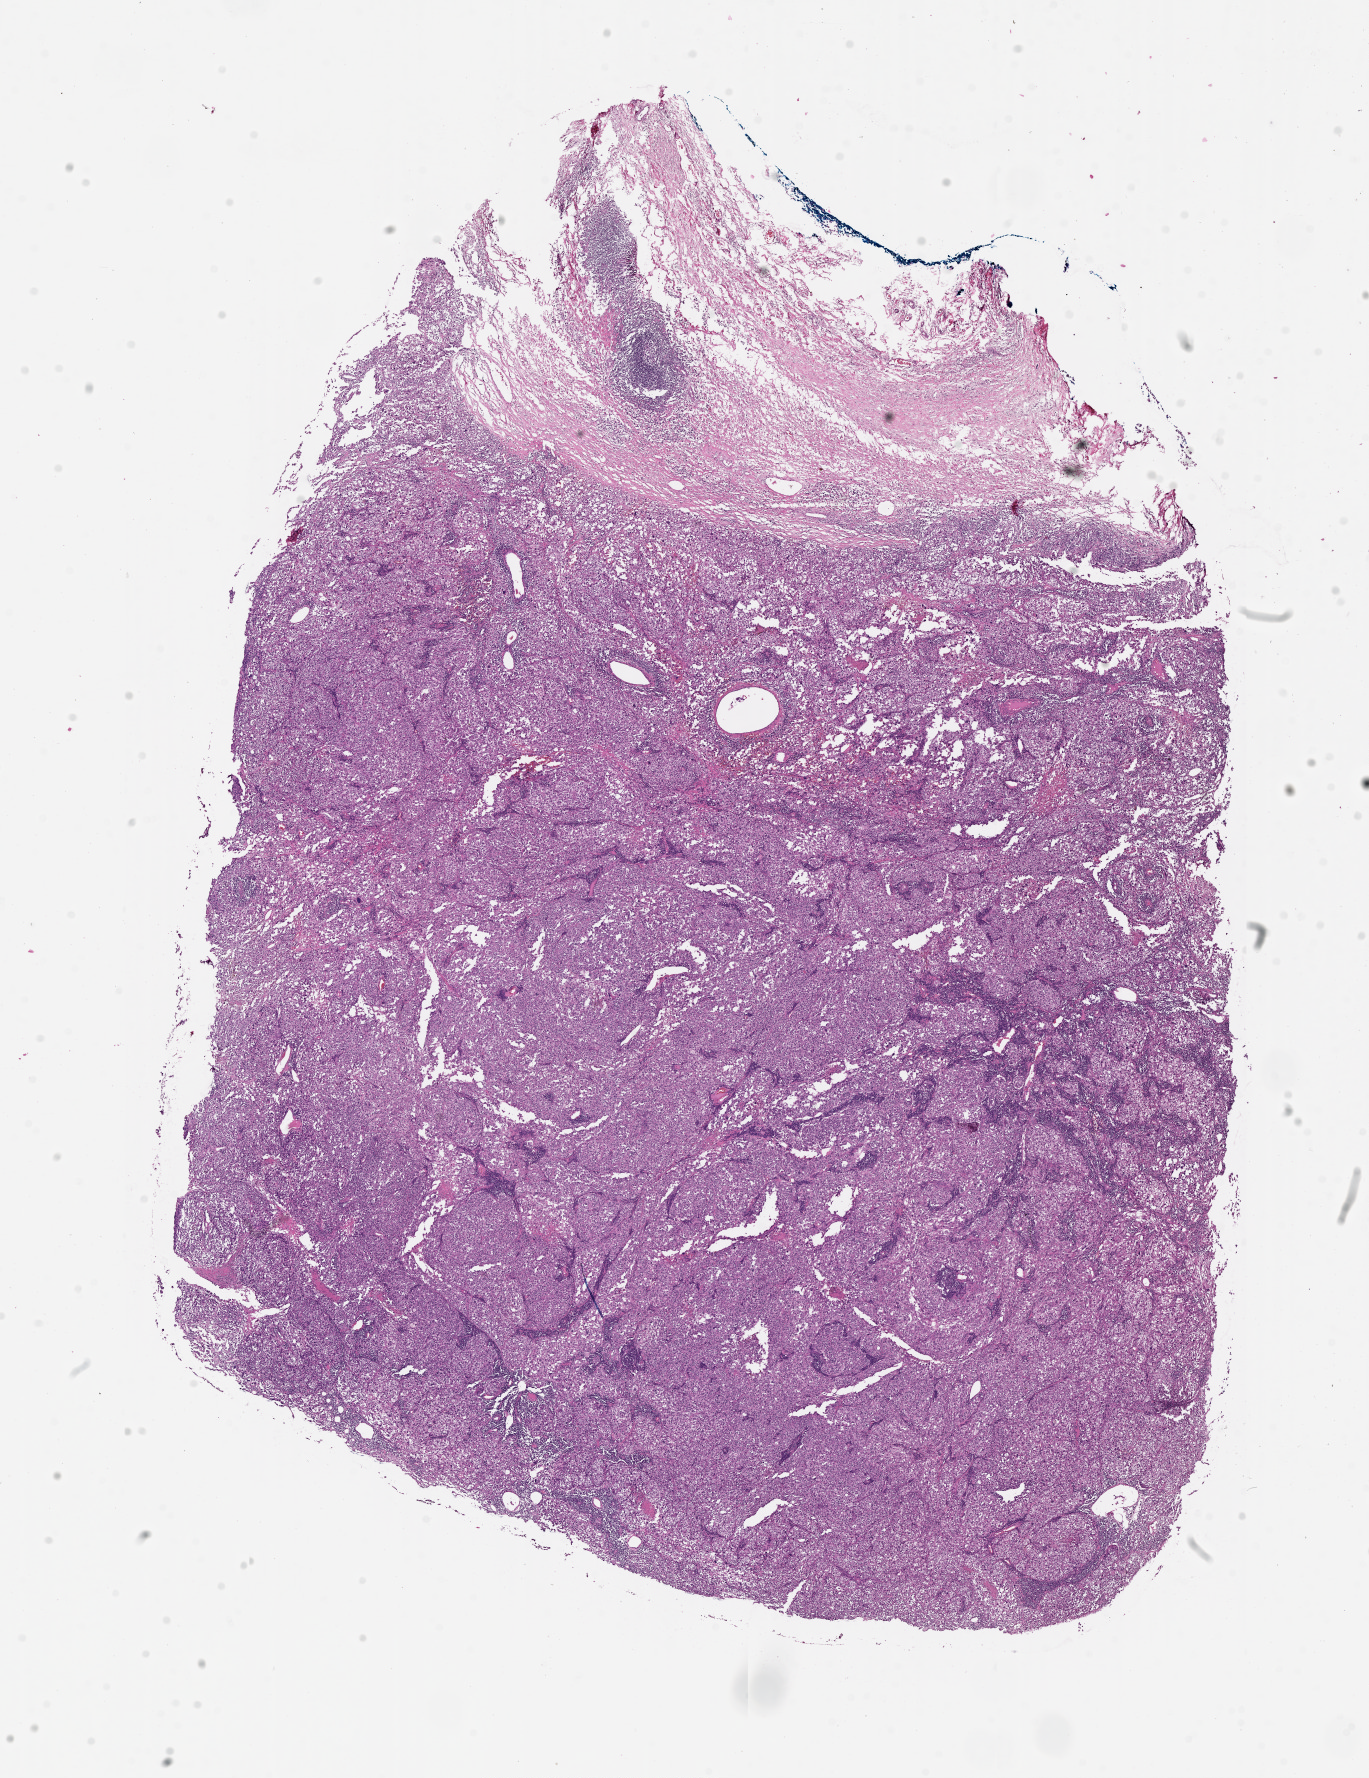
Digitized H&E tissue section (whole slide) — a low-resolution overview of the entire scanned area, about 11.0 x 14.3 mm (slide scanned at 20x). Female, 54 y/o.
Patient diagnosis: Malignant melanoma, NOS.